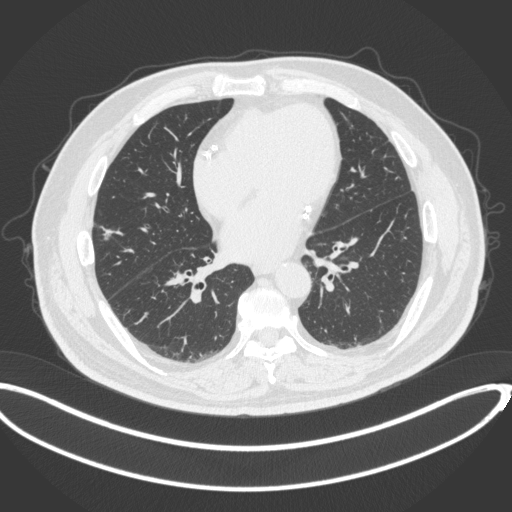
Chest CT, one axial slice; position 138 of 342 along the scan axis; reconstruction kernel B31f; lung window (W 1500 / L -600 HU); 1 mm slice thickness; 512 × 512 image matrix, field of view 427 × 427 mm. Male patient, age 68 years. Case-level facts recorded for this patient, not image findings: clinical TNM (as recorded): T1c N0 M0; histopathological grade: G2.
Annotated regions visible in this slice (bounding box drawn by a radiologist):
- lung tumour (recorded histology: adenocarcinoma): box from (x=101, y=226) to (x=115, y=243) px